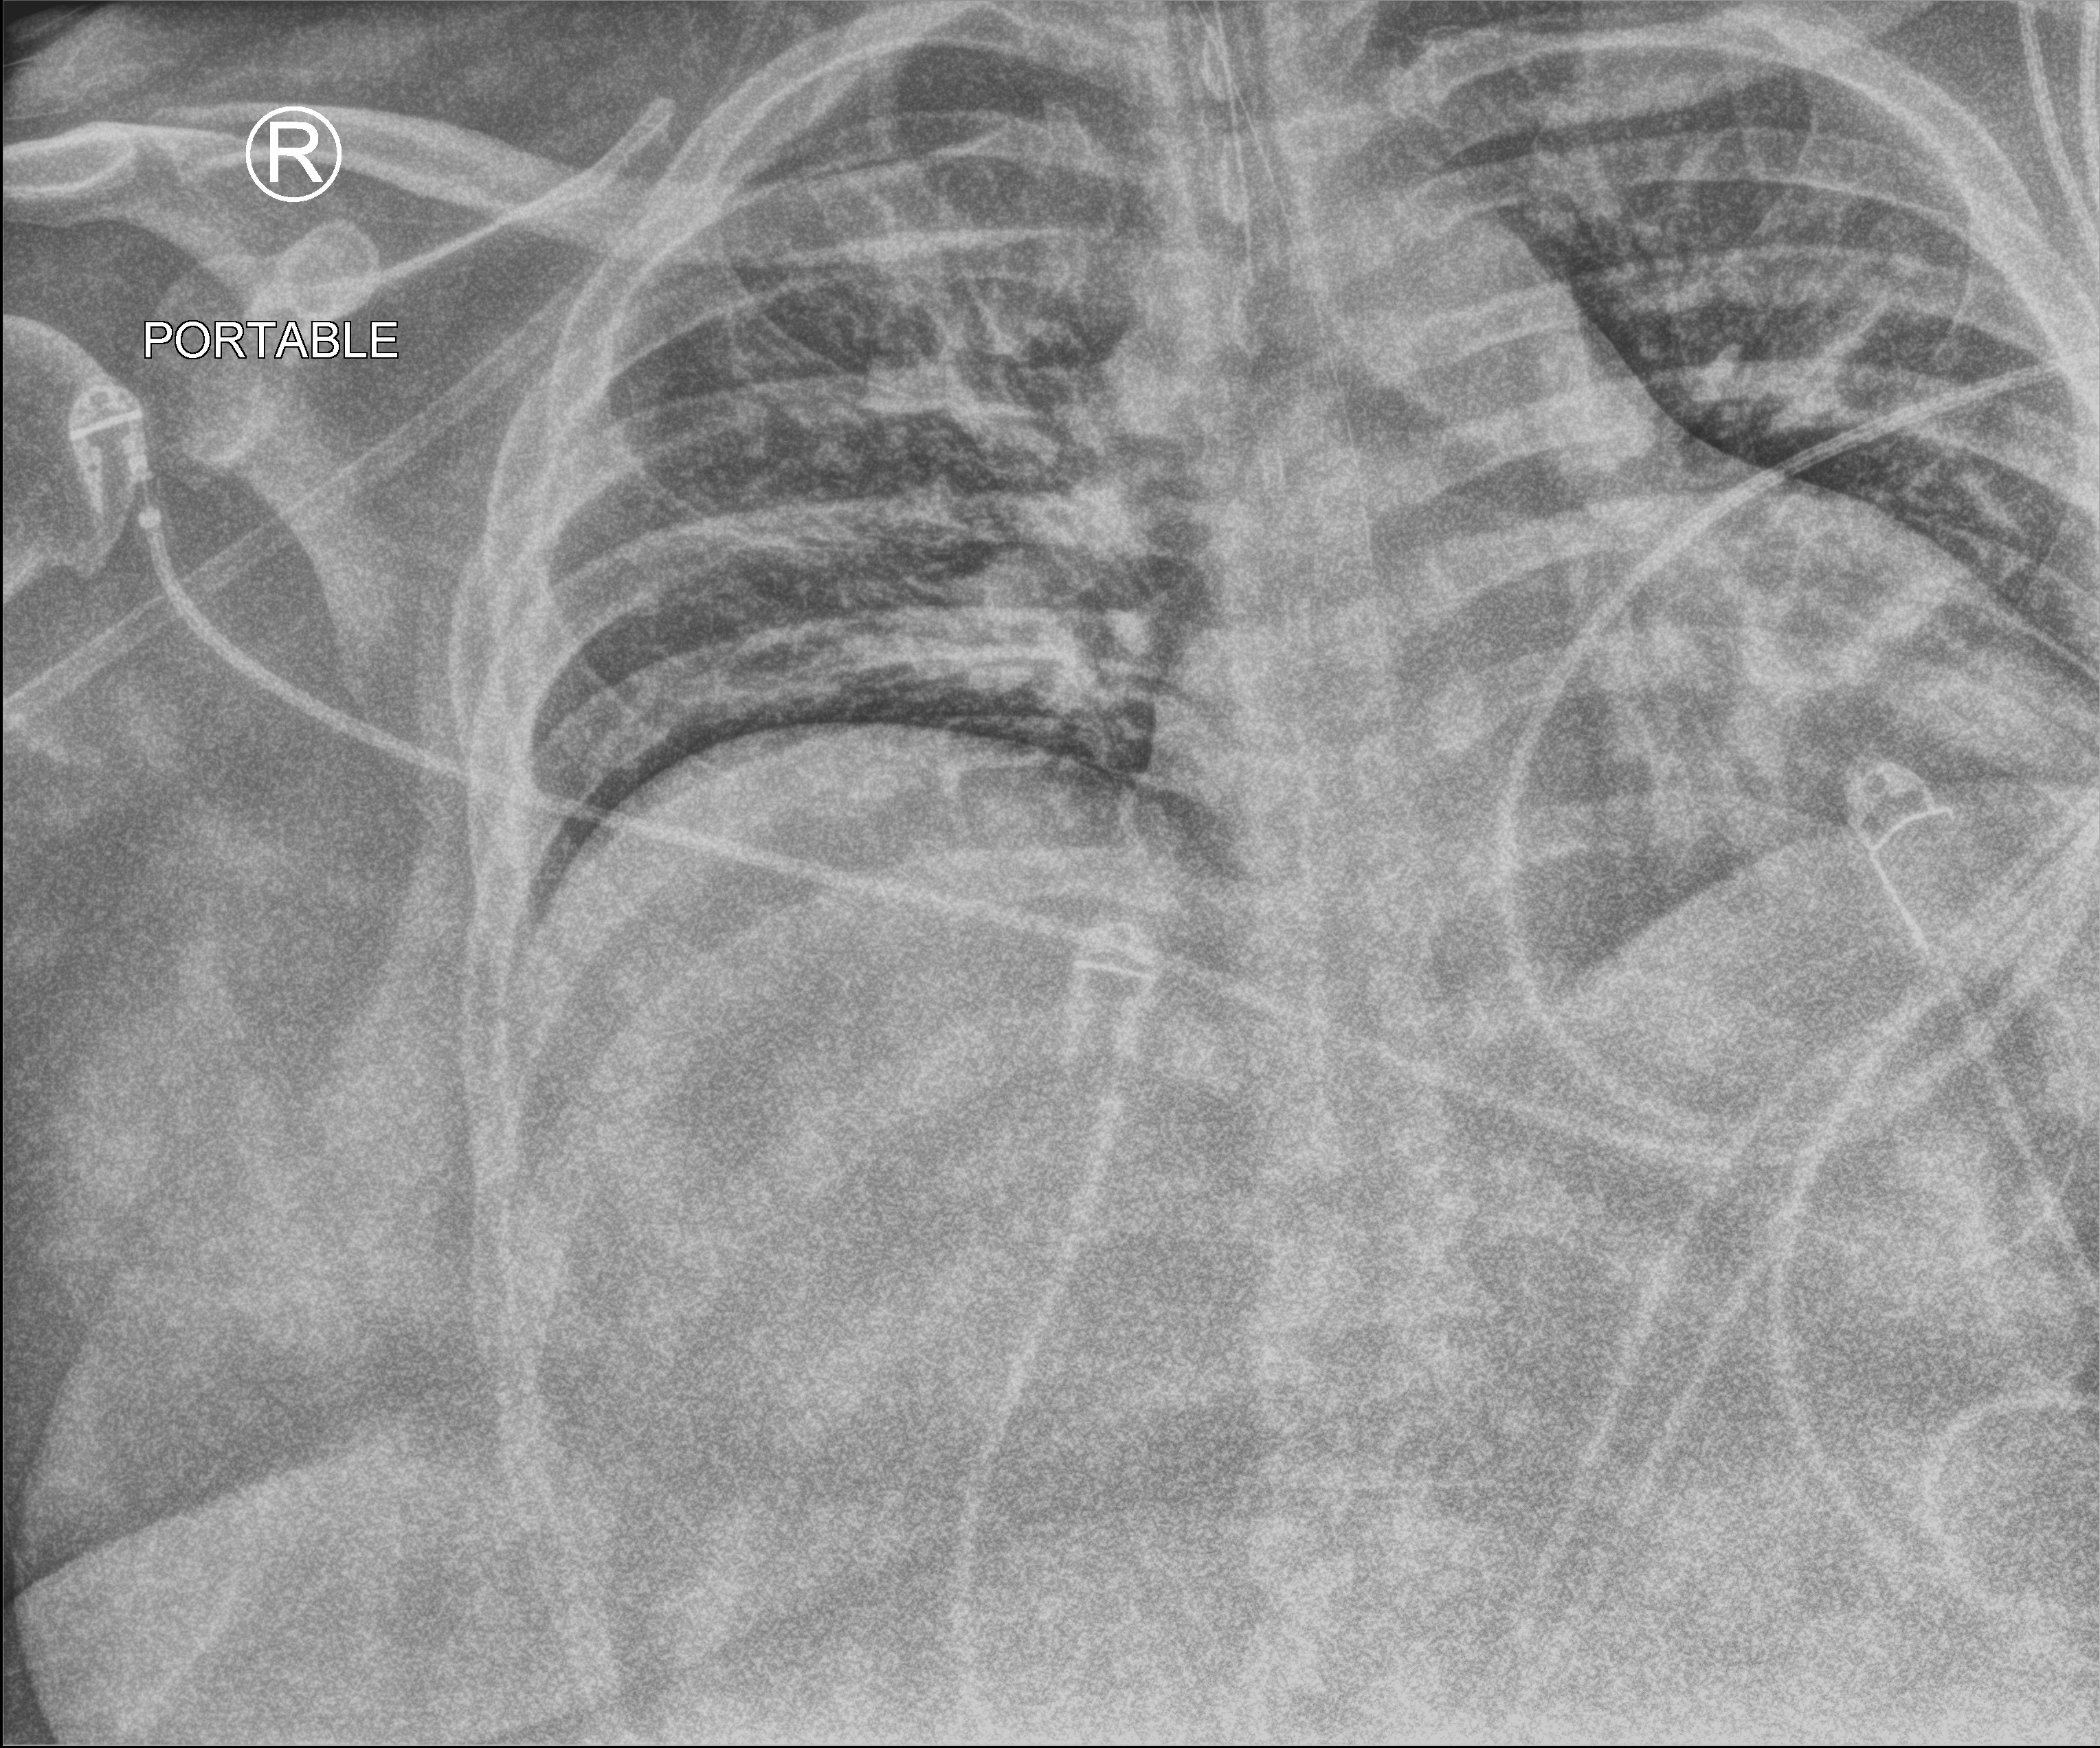
Chest X-ray (portable); anteroposterior (AP) projection. Male patient hospitalised with COVID-19, age 18–59 years.
From the hospital-stay record, not from the radiograph (when in the stay this image was taken is not recorded): admitted to intensive care during this hospital stay: yes; mechanically ventilated during this hospital stay: yes.